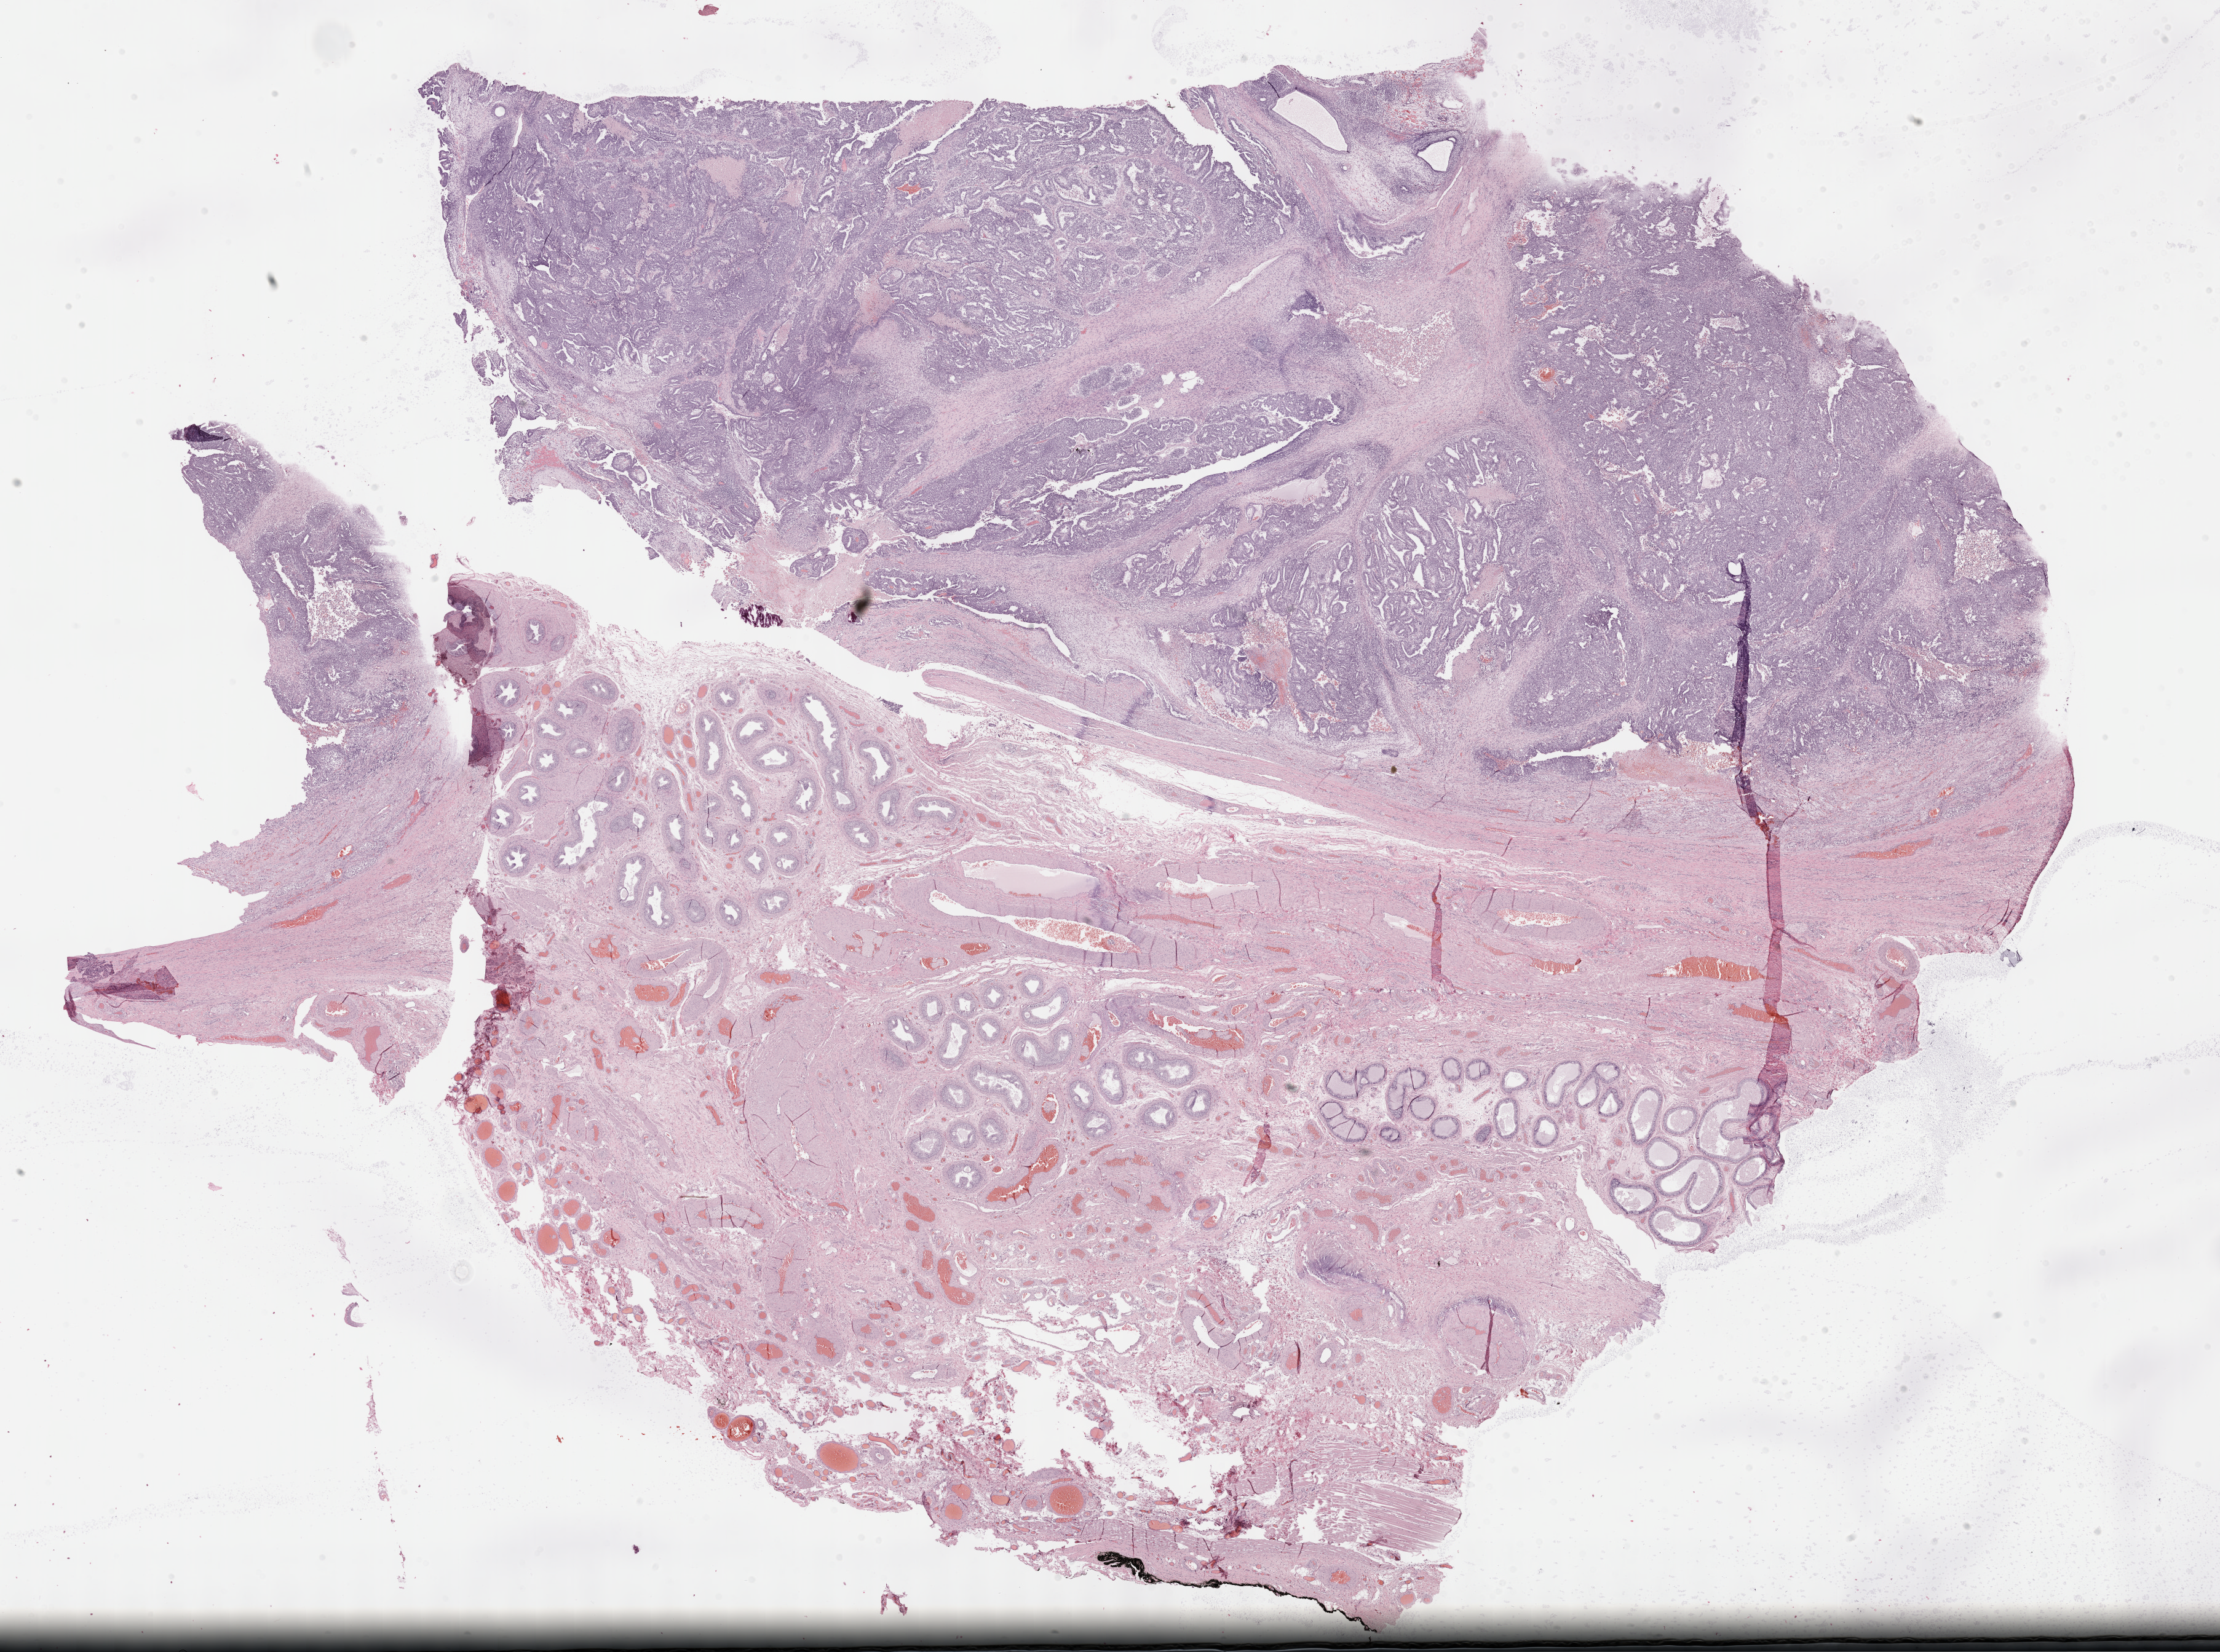
Hematoxylin and eosin (H&E) stained whole-slide image, a low-resolution overview of the entire scanned area, about 29.2 x 21.7 mm, FFPE section, primary tumour sample from the testis. Male patient; age at initial diagnosis 18 years.
Pathologic diagnosis: Embryonal carcinoma, NOS. AJCC pathologic stage: IA (7th edition).